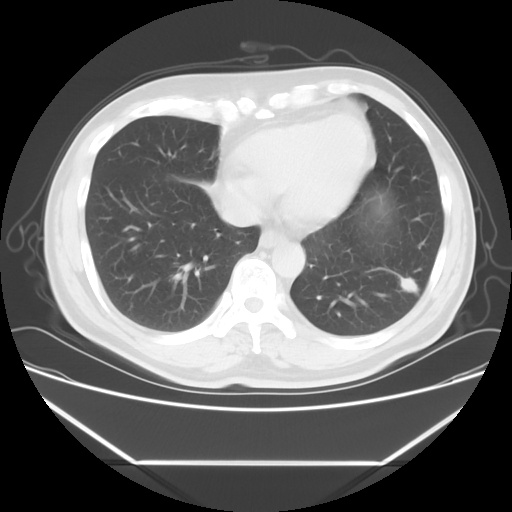
Chest CT, one axial slice; position 19 of 57 along the scan axis; reconstruction kernel STANDARD; lung window (W 1500 / L -600 HU); 512 × 512 image matrix, field of view 384 × 384 mm. Male patient, age 53 years. From the clinical record (not read from this slice): clinical TNM (as recorded): T1c N0 M0.
Annotated regions visible in this slice (rectangle marked by the reading radiologist):
- lung tumour (recorded histology: adenocarcinoma): bounding box (x1, y1, x2, y2) in pixels: (384, 262, 430, 311)